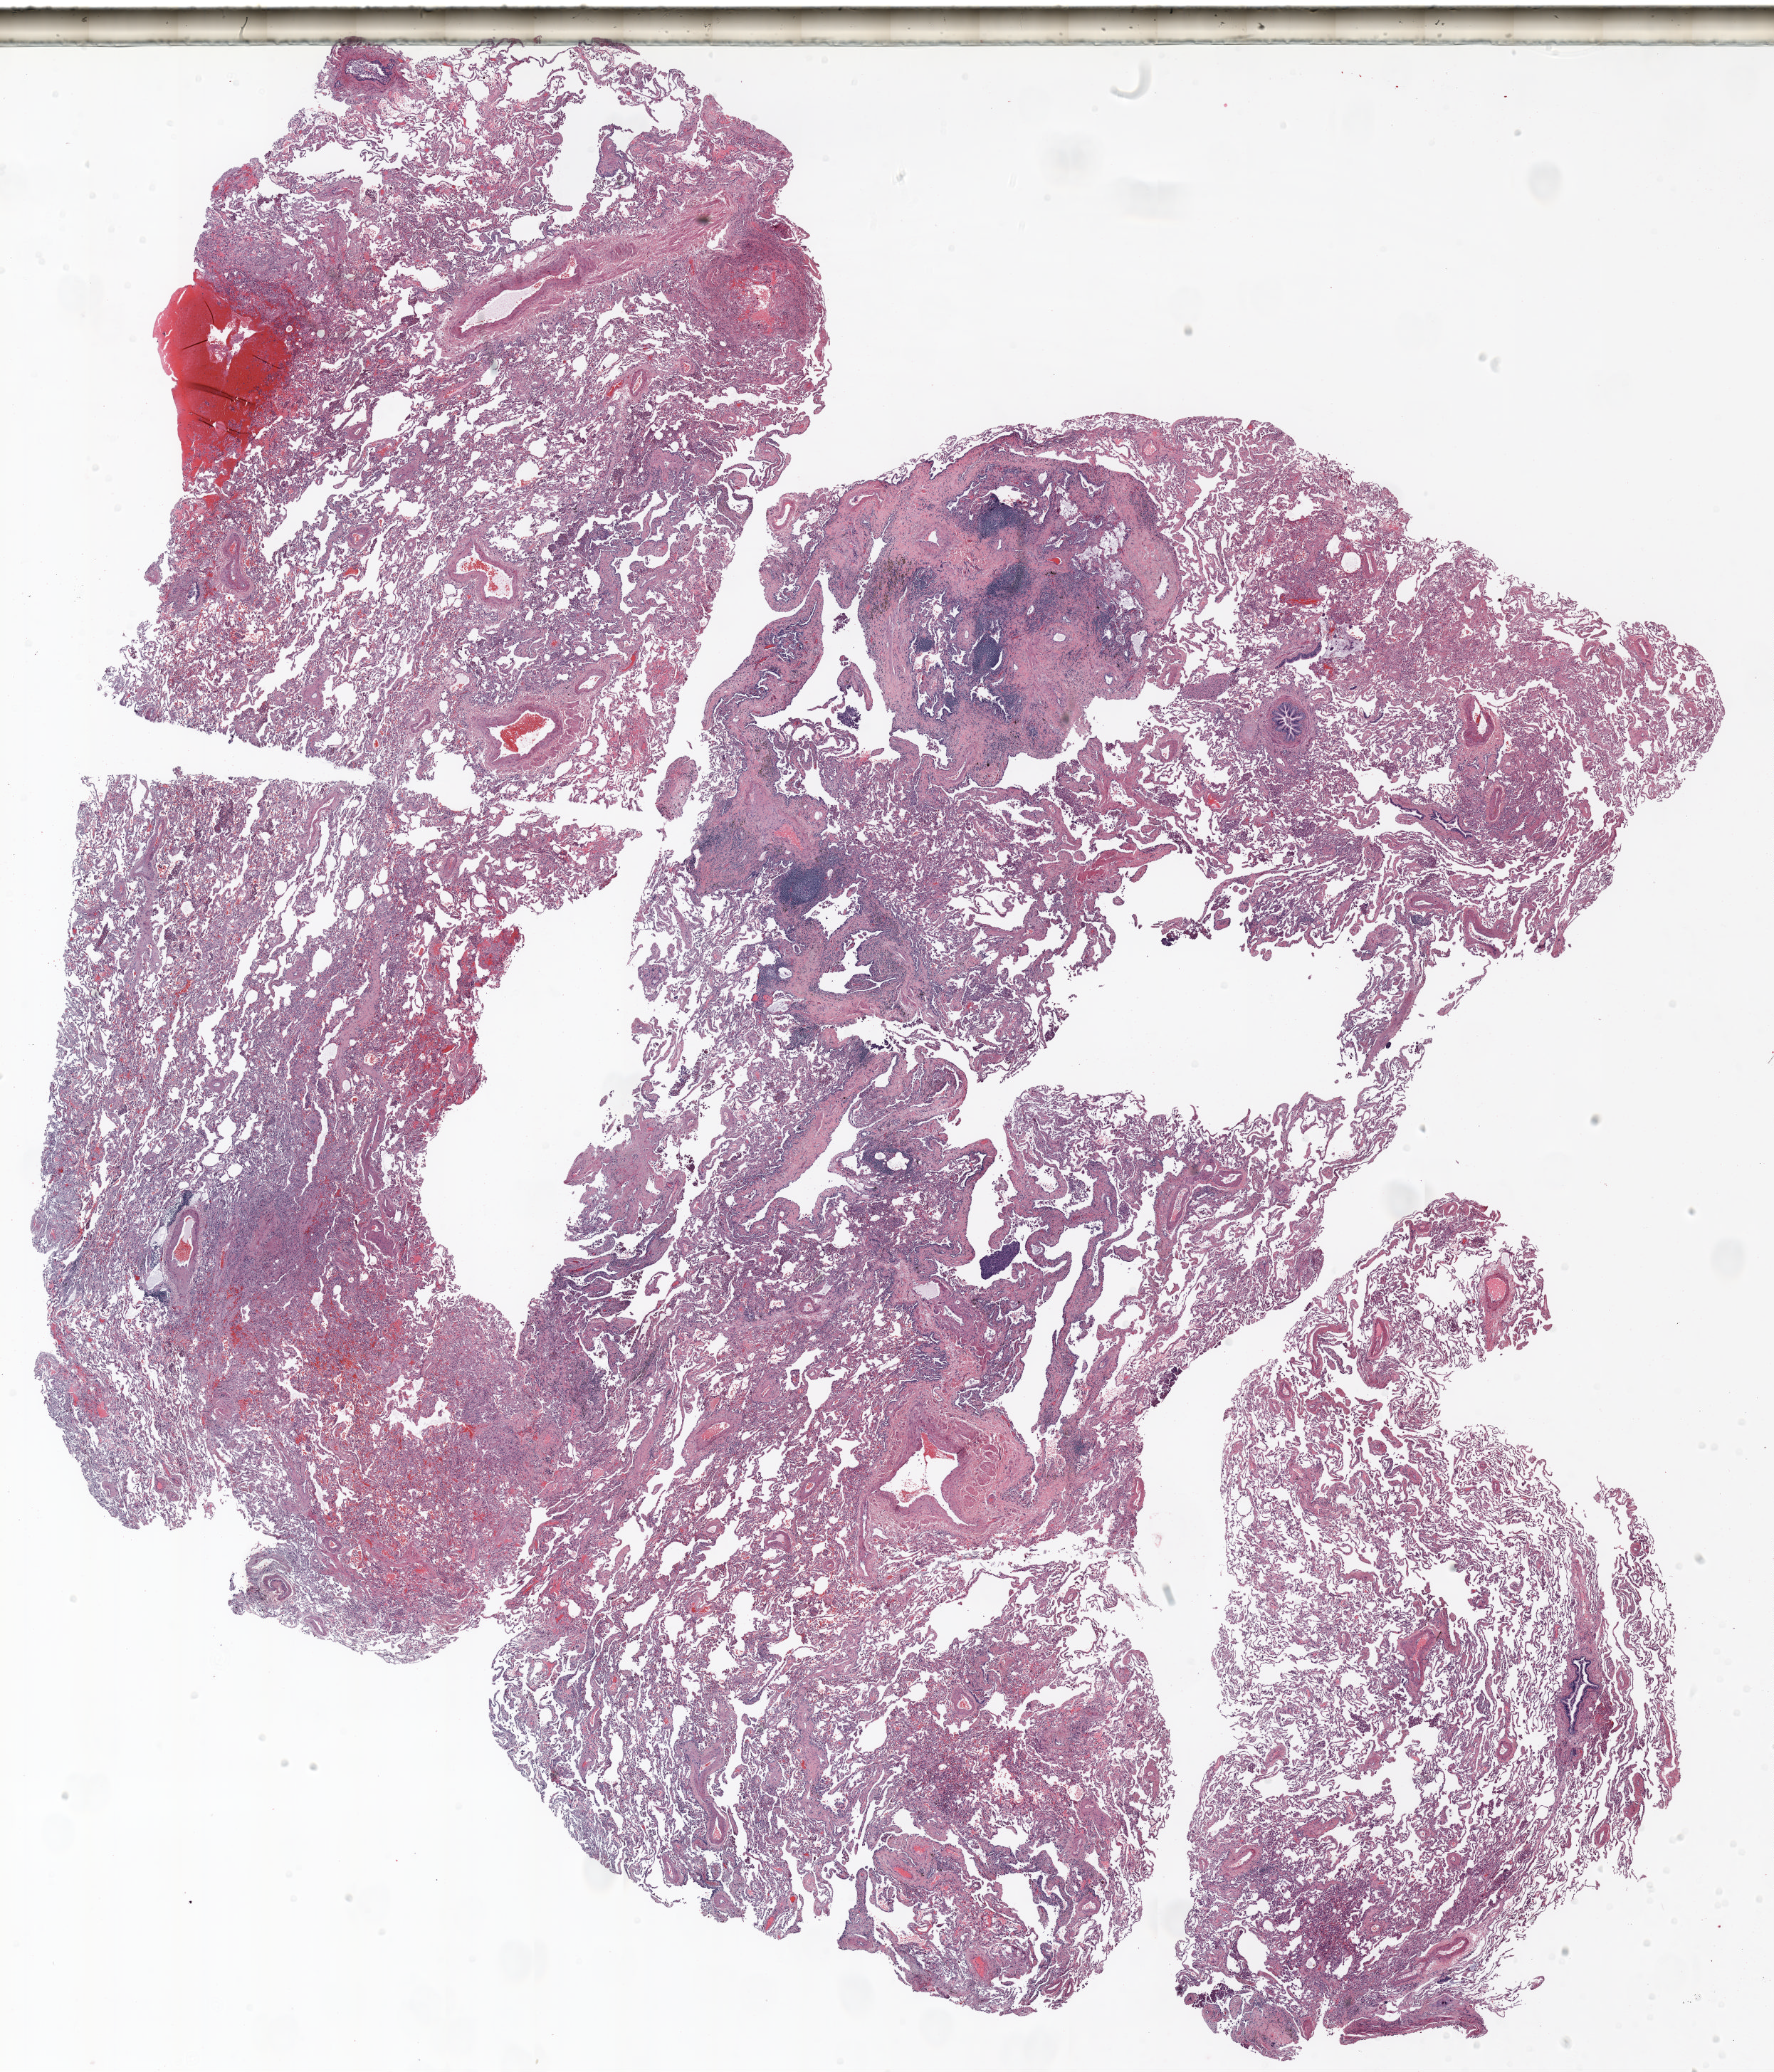
Hematoxylin and eosin (H&E) stained whole-slide image, shown as a low-resolution overview of the whole scanned area (about 20.0 x 23.4 mm); formalin-fixed paraffin-embedded (FFPE) section; lung tissue. Male, age 62 at enrolment. Grade: moderately differentiated (G2).
Stage (AJCC 6th edition): IA. Primary tumour location (clinical record): right upper lobe. Participant's lung-cancer diagnosis: Adenocarcinoma, NOS (ICD-O-3 8140/3). Tumour size (pathology): 16 mm.